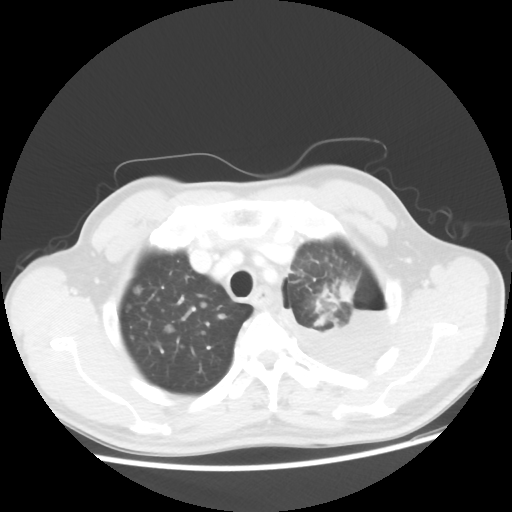
Chest CT, one axial slice. Position 41 of 48 along the scan axis. Reconstruction kernel STANDARD. 100 kVp. Lung window (W 1500 / L -600 HU). 5 mm slice thickness. 512 × 512 image matrix, field of view 362 × 362 mm. Male patient, age 55 years. Case-level facts recorded for this patient, not image findings: clinical TNM (as recorded): T2 N3 M1a.
Annotated regions visible in this slice (rectangle marked by the reading radiologist):
- lung tumour (recorded histology: squamous cell carcinoma): bounding box [x1, y1, x2, y2] px = [331, 280, 361, 310]